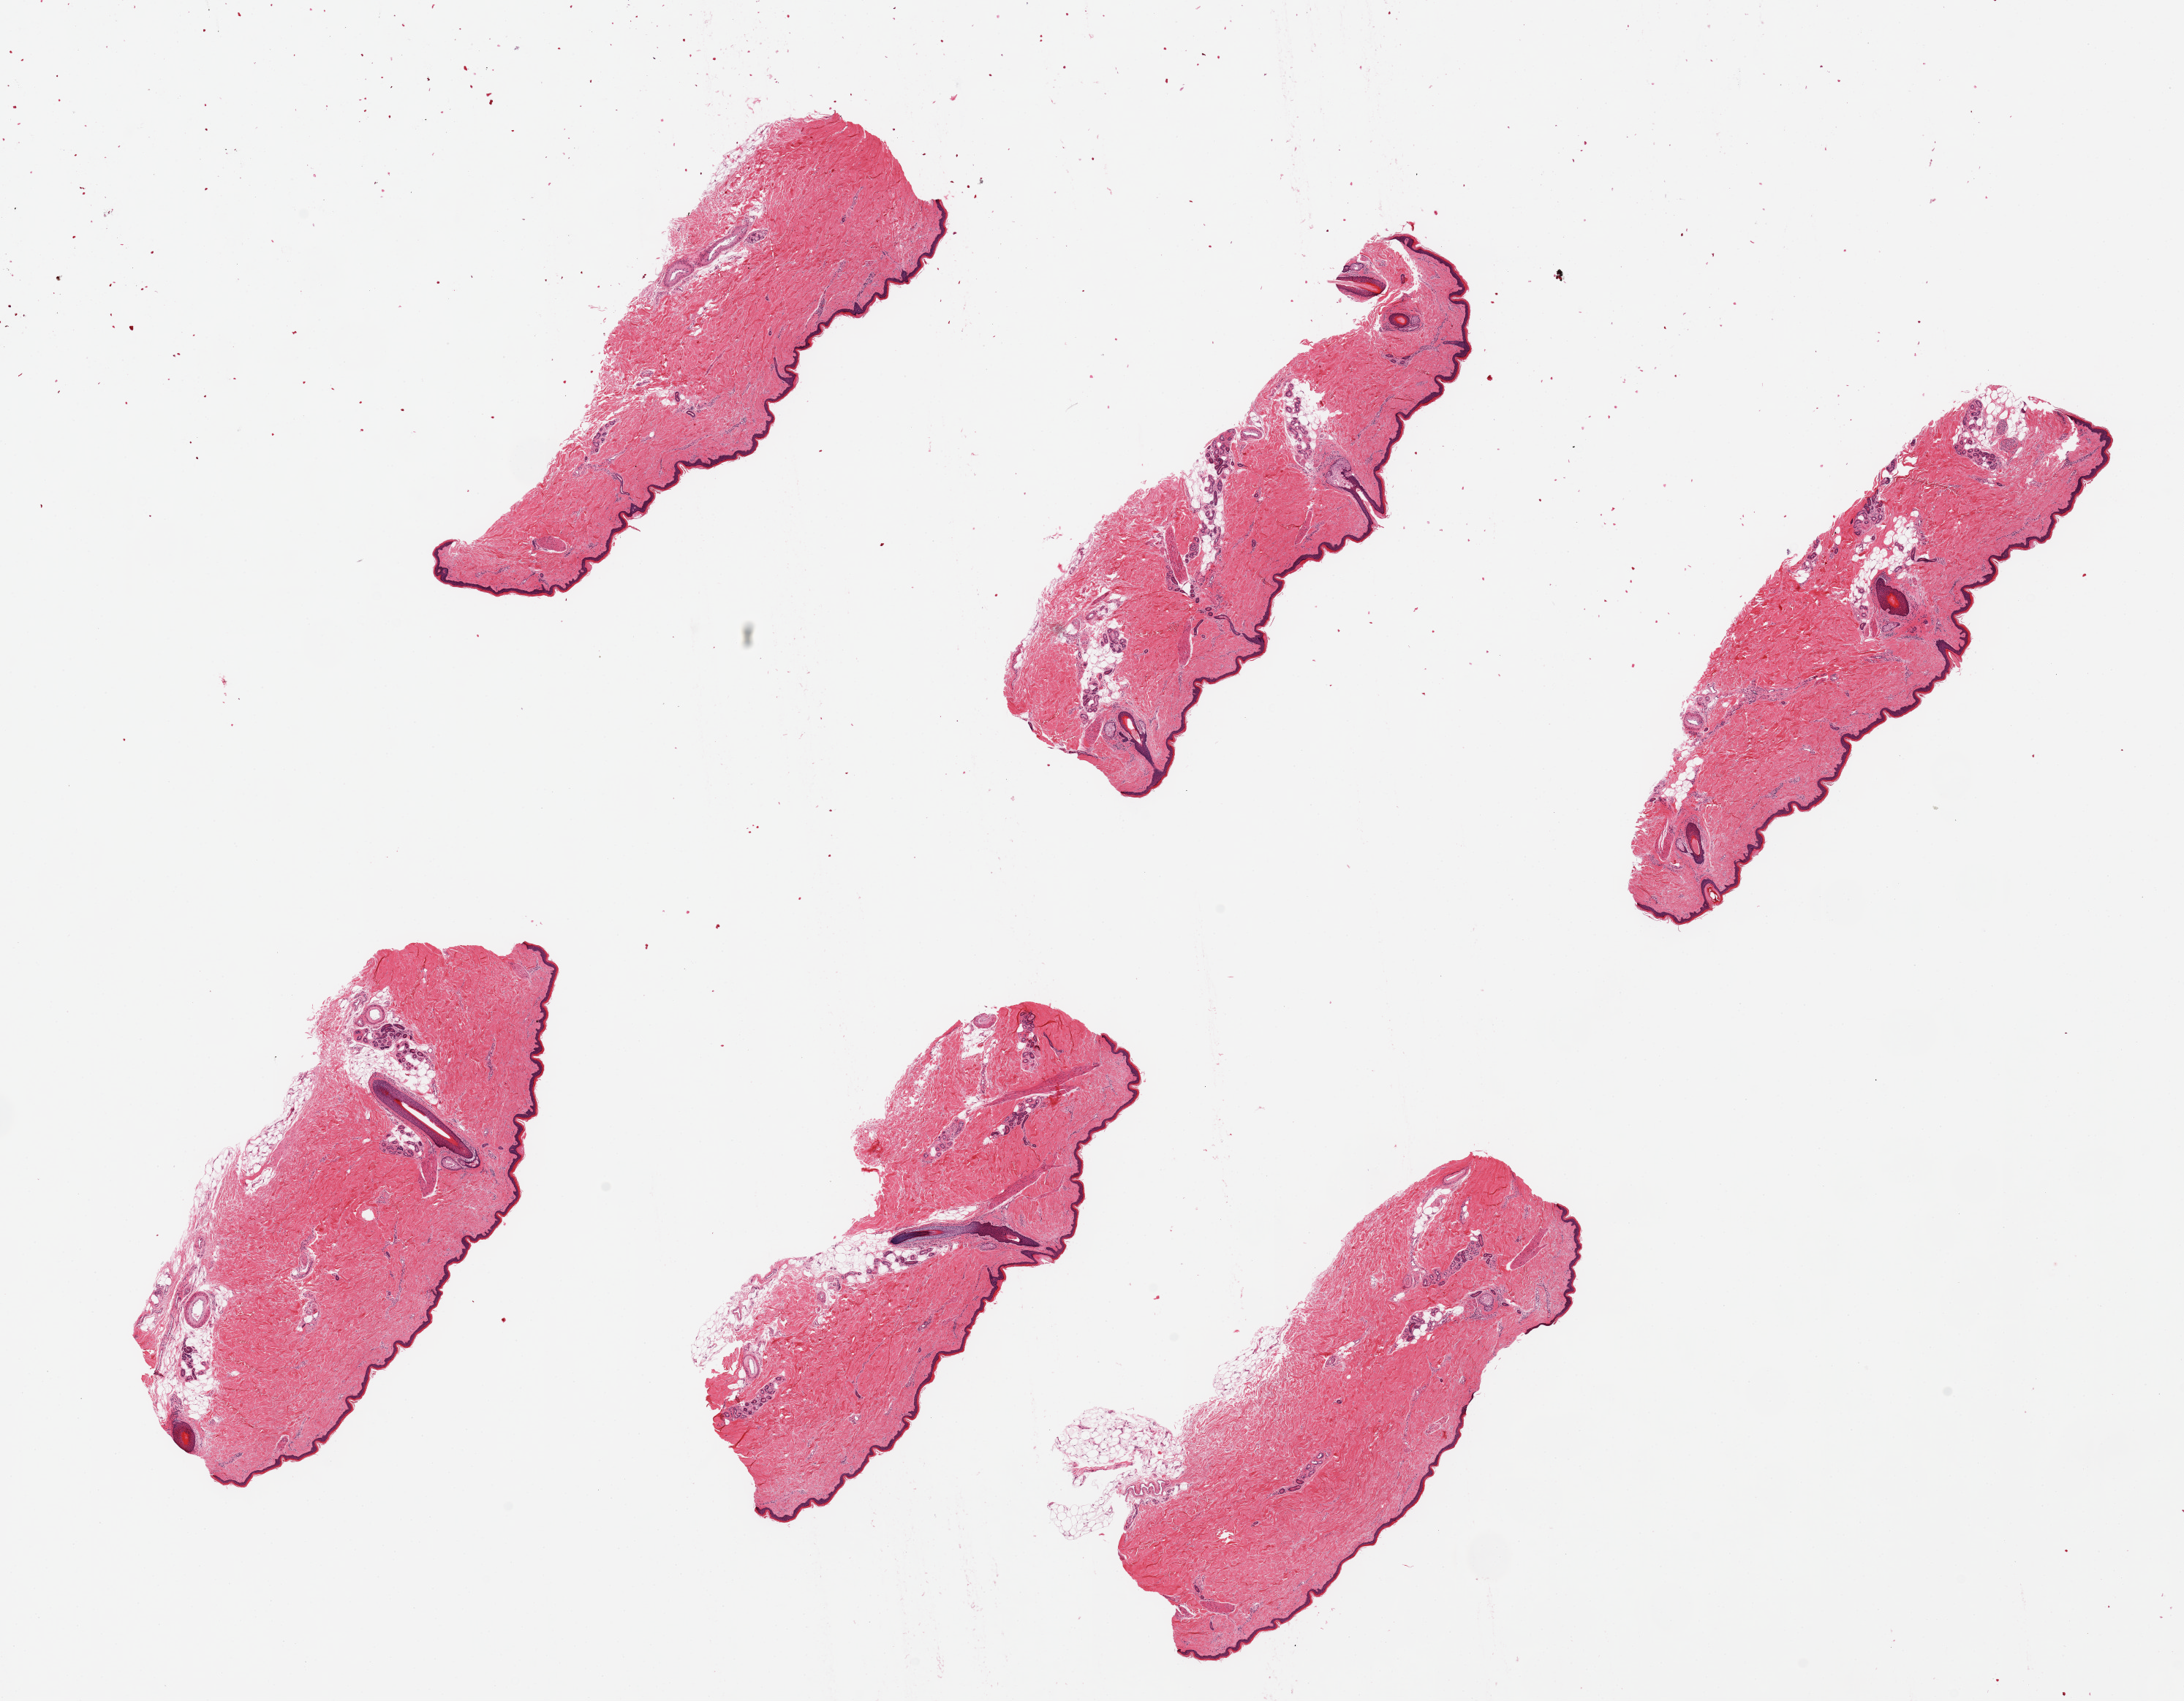
Hematoxylin and eosin (H&E) whole-slide image, brightfield — whole scanned area (about 23.6 x 18.4 mm) shown as a low-resolution overview; PAXgene-fixed, paraffin-embedded tissue; section of skin of lower leg (target tissue); donor tissue sample. Donor sex: male.
Reviewer comment on this tissue sample: 6 pieces, up to 7x2mm; squamous epitheiium is ~2% of thickness.